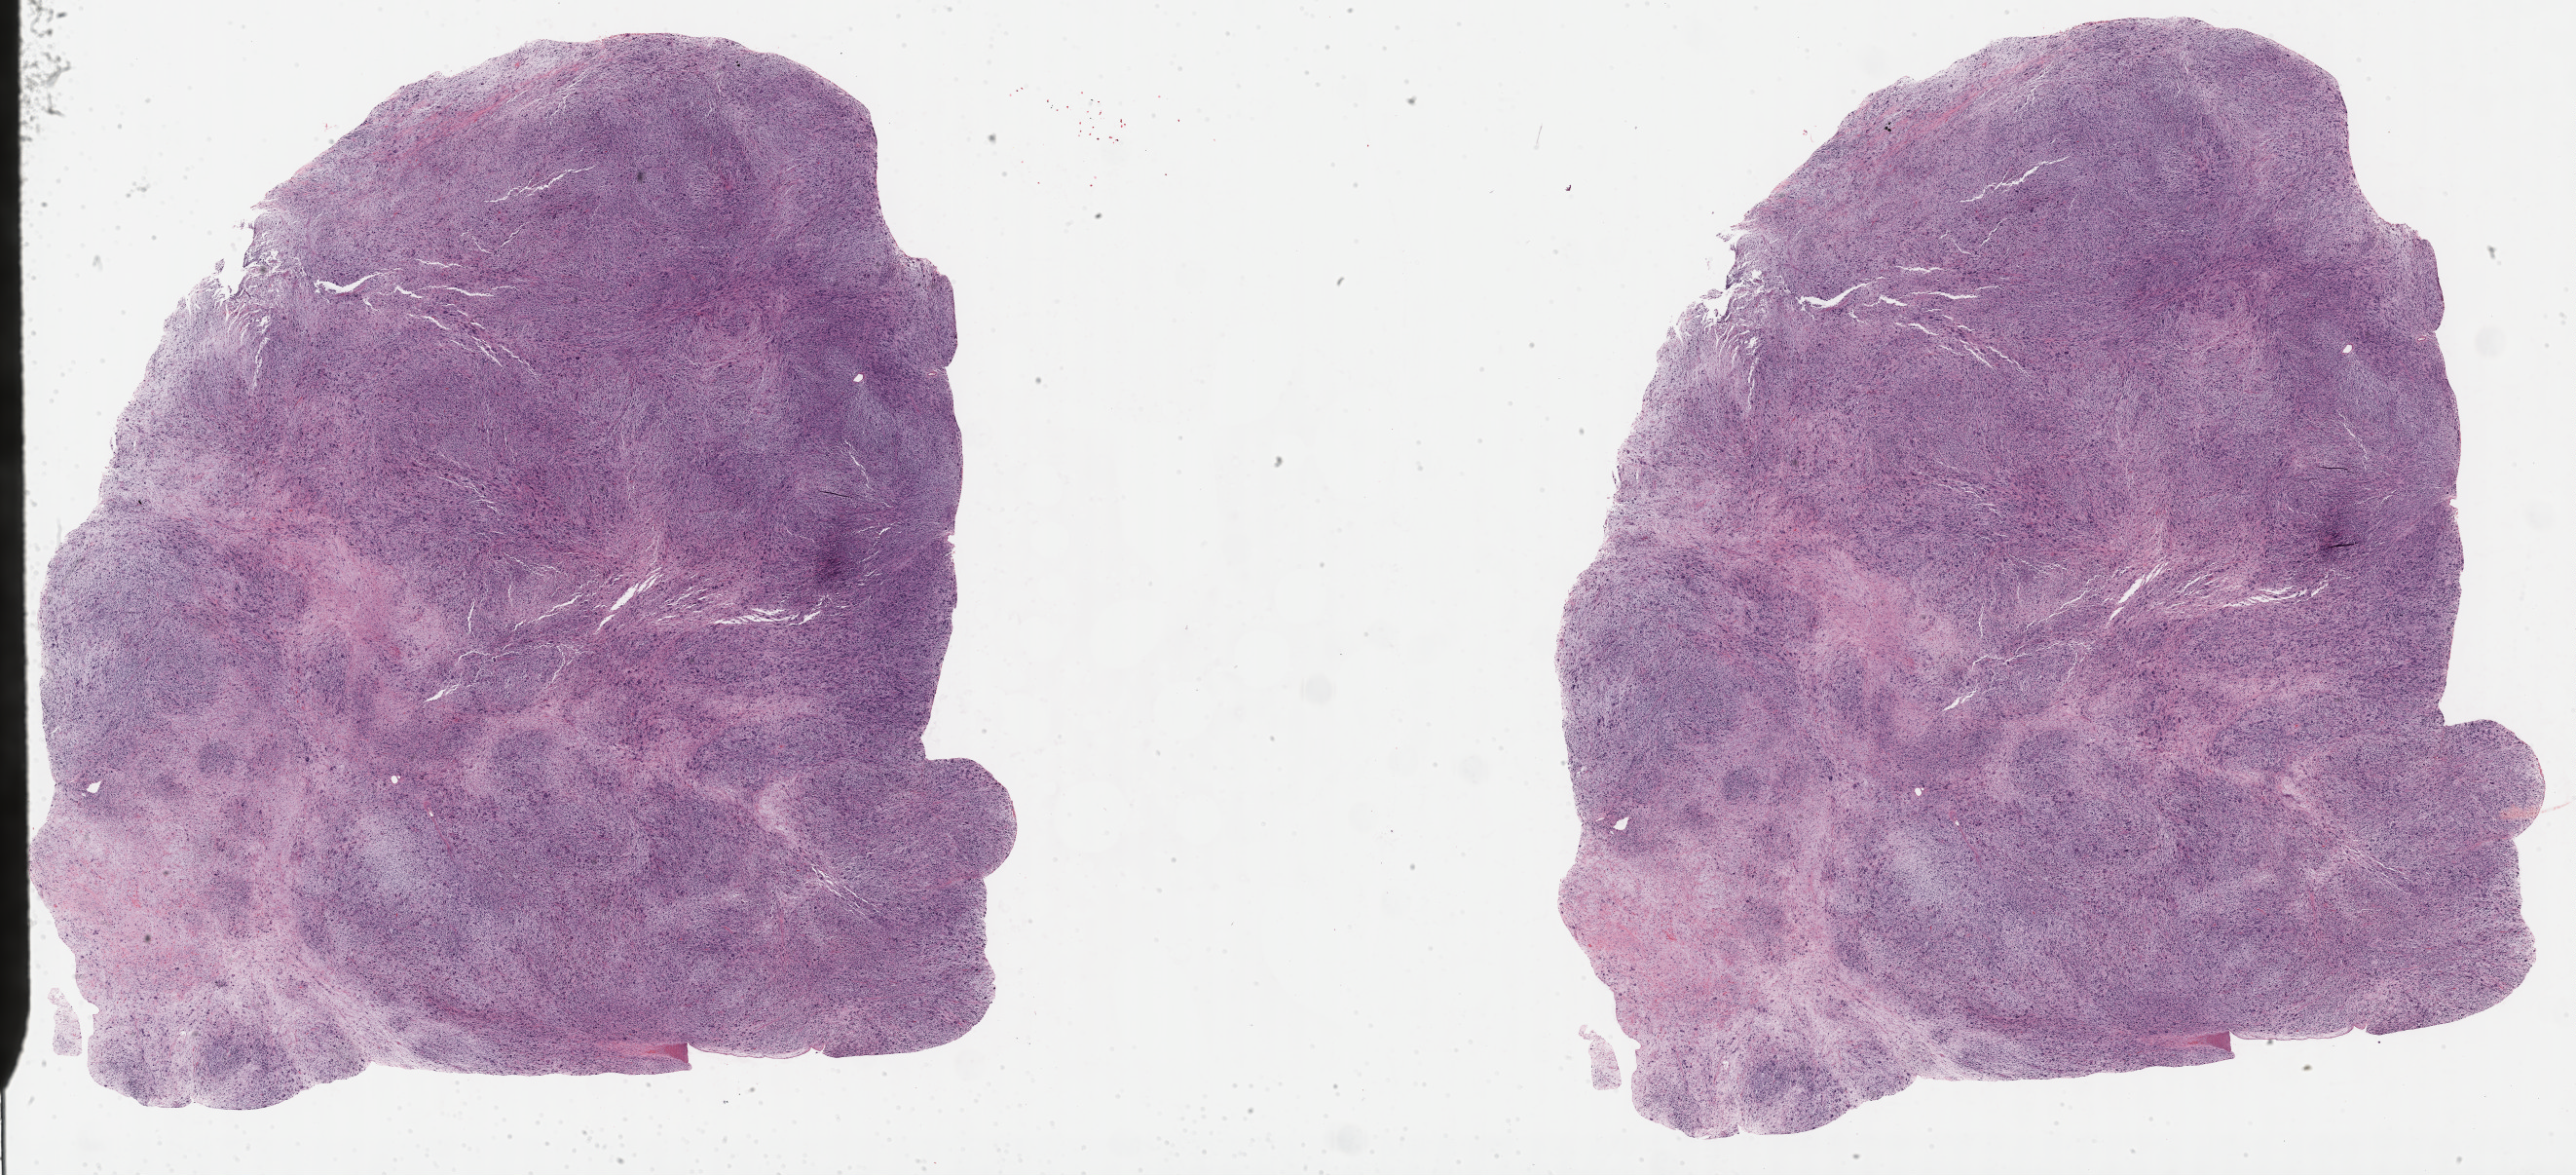
H&E whole-slide image — shown as a low-resolution overview of the whole scanned area (about 42.8 x 19.5 mm, slide scanned at 40x), formalin-fixed paraffin-embedded (FFPE) diagnostic section, primary tumour sample from the connective, subcutaneous and other soft tissues. Patient: female, age at initial diagnosis 78 years.
Histologic diagnosis: Malignant fibrous histiocytoma (connective, subcutaneous and other soft tissues of lower limb and hip).